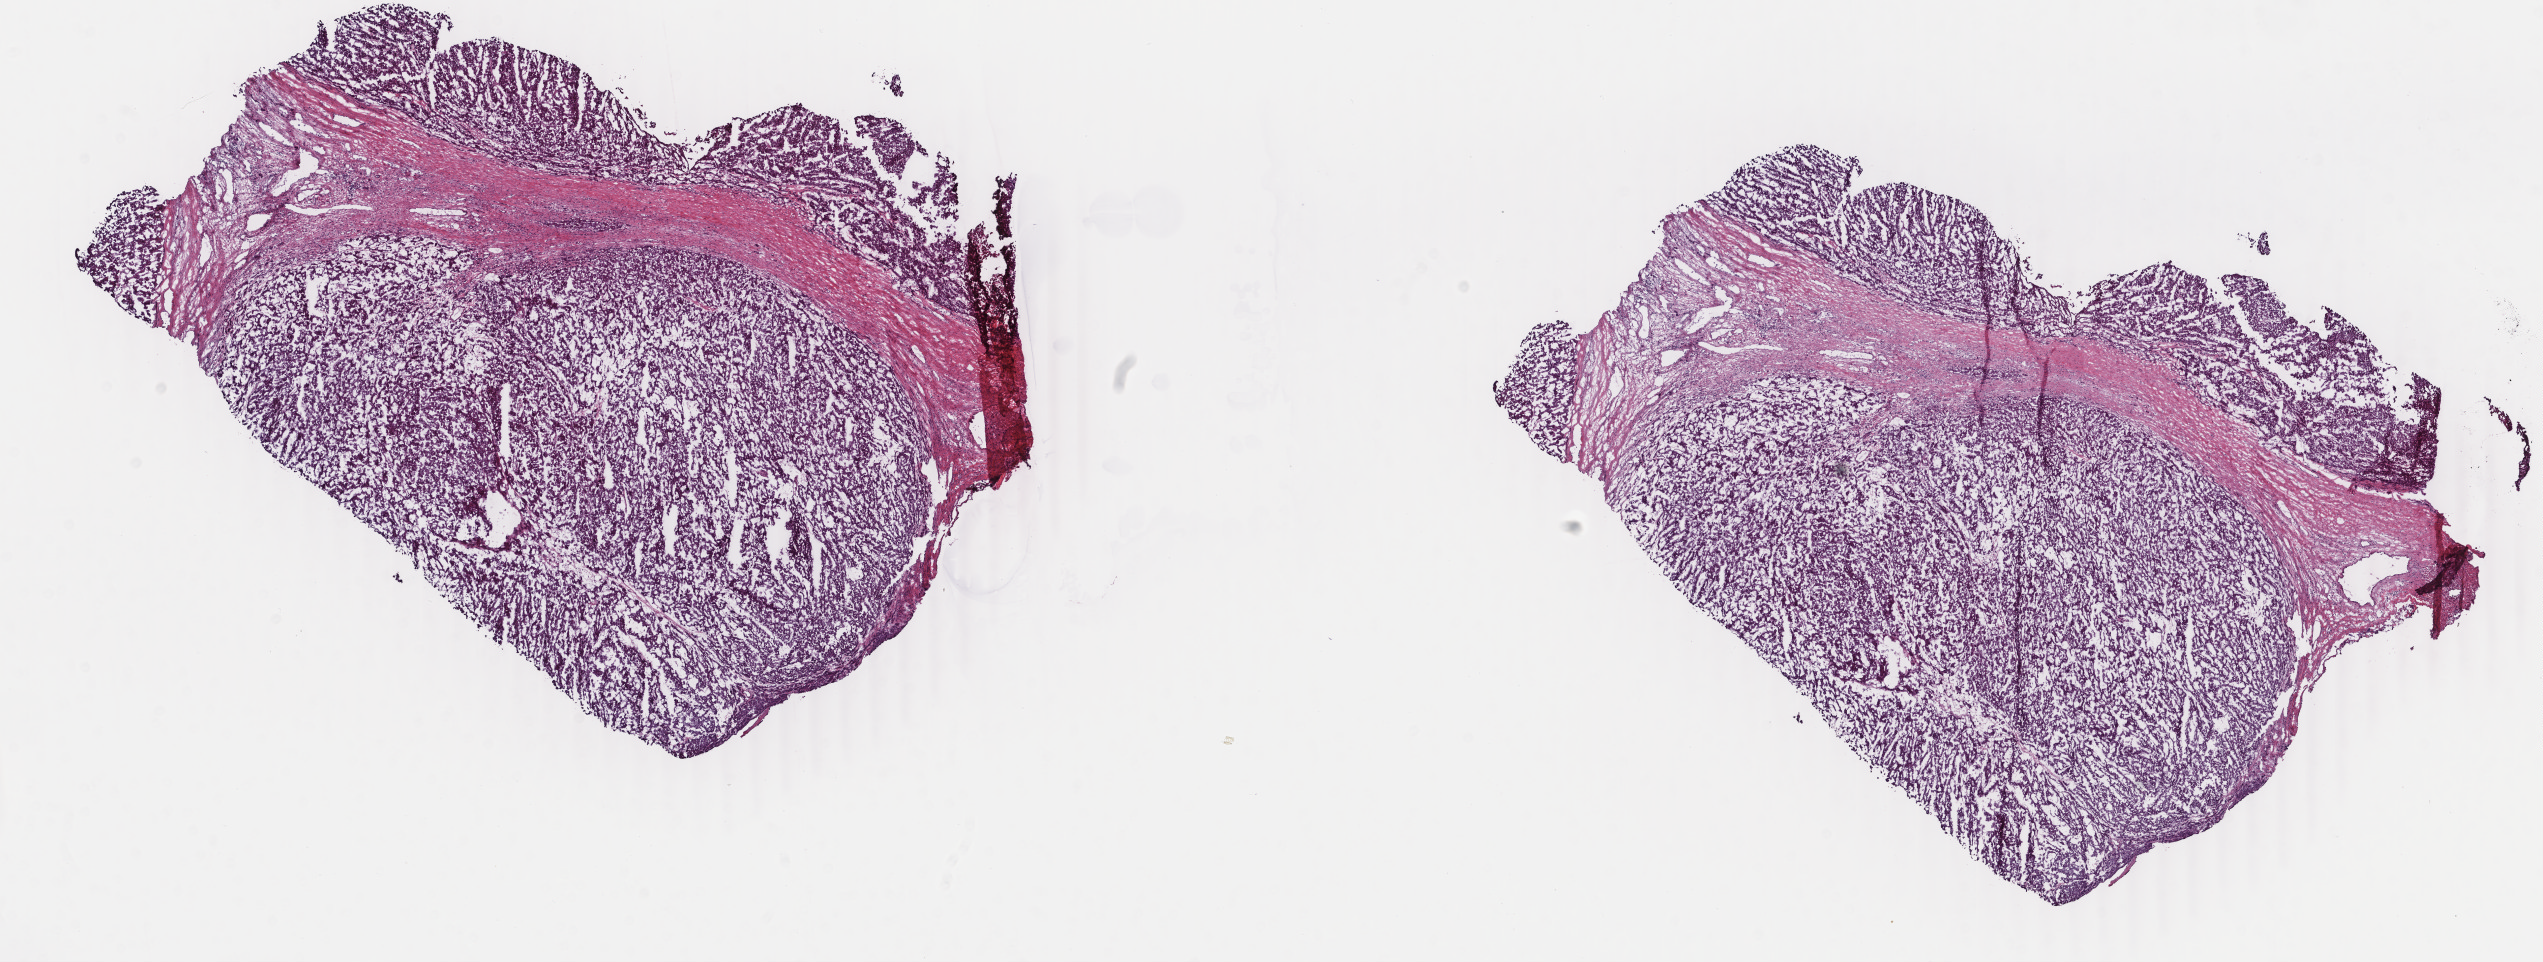
Digitized H&E tissue section (whole slide) — shown as a low-resolution overview of the whole scanned area (about 20.2 x 7.7 mm, slide scanned at 40x). Frozen section from the top of the tissue portion. Primary tumour sample from the liver. Male, age 76 years at initial diagnosis. Histologic grade: G1 (well differentiated). Pathologist review of this section (percent, as recorded): tumour cells 85%, tumour nuclei 90%, normal cells 0%, stromal cells 15%, necrosis 0%. Infiltration values recorded for this section: lymphocyte infiltration 0%, monocyte infiltration 0%, neutrophil infiltration 0%.
Diagnosis: Hepatocellular carcinoma, NOS.